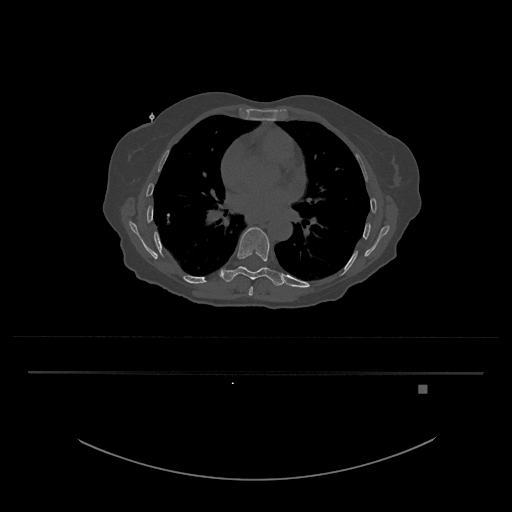
CT including the spine, one axial slice; reconstruction kernel Br40s/3; 120 kVp; bone window (W 1800 / L 400 HU); 0.5 mm slice thickness; 512 × 512 image matrix, field of view 500 × 500 mm. Female patient, age 57 years. Case-level facts recorded for this patient, not image findings: primary cancer: cervical.
Outlined on this slice (semi-automatic segmentation, software-assisted and operator-edited):
- T8 vertebra: bounding box <248,286,253,296> (left, top, right, bottom; pixels)
- T9 vertebra: <221,227,285,286>